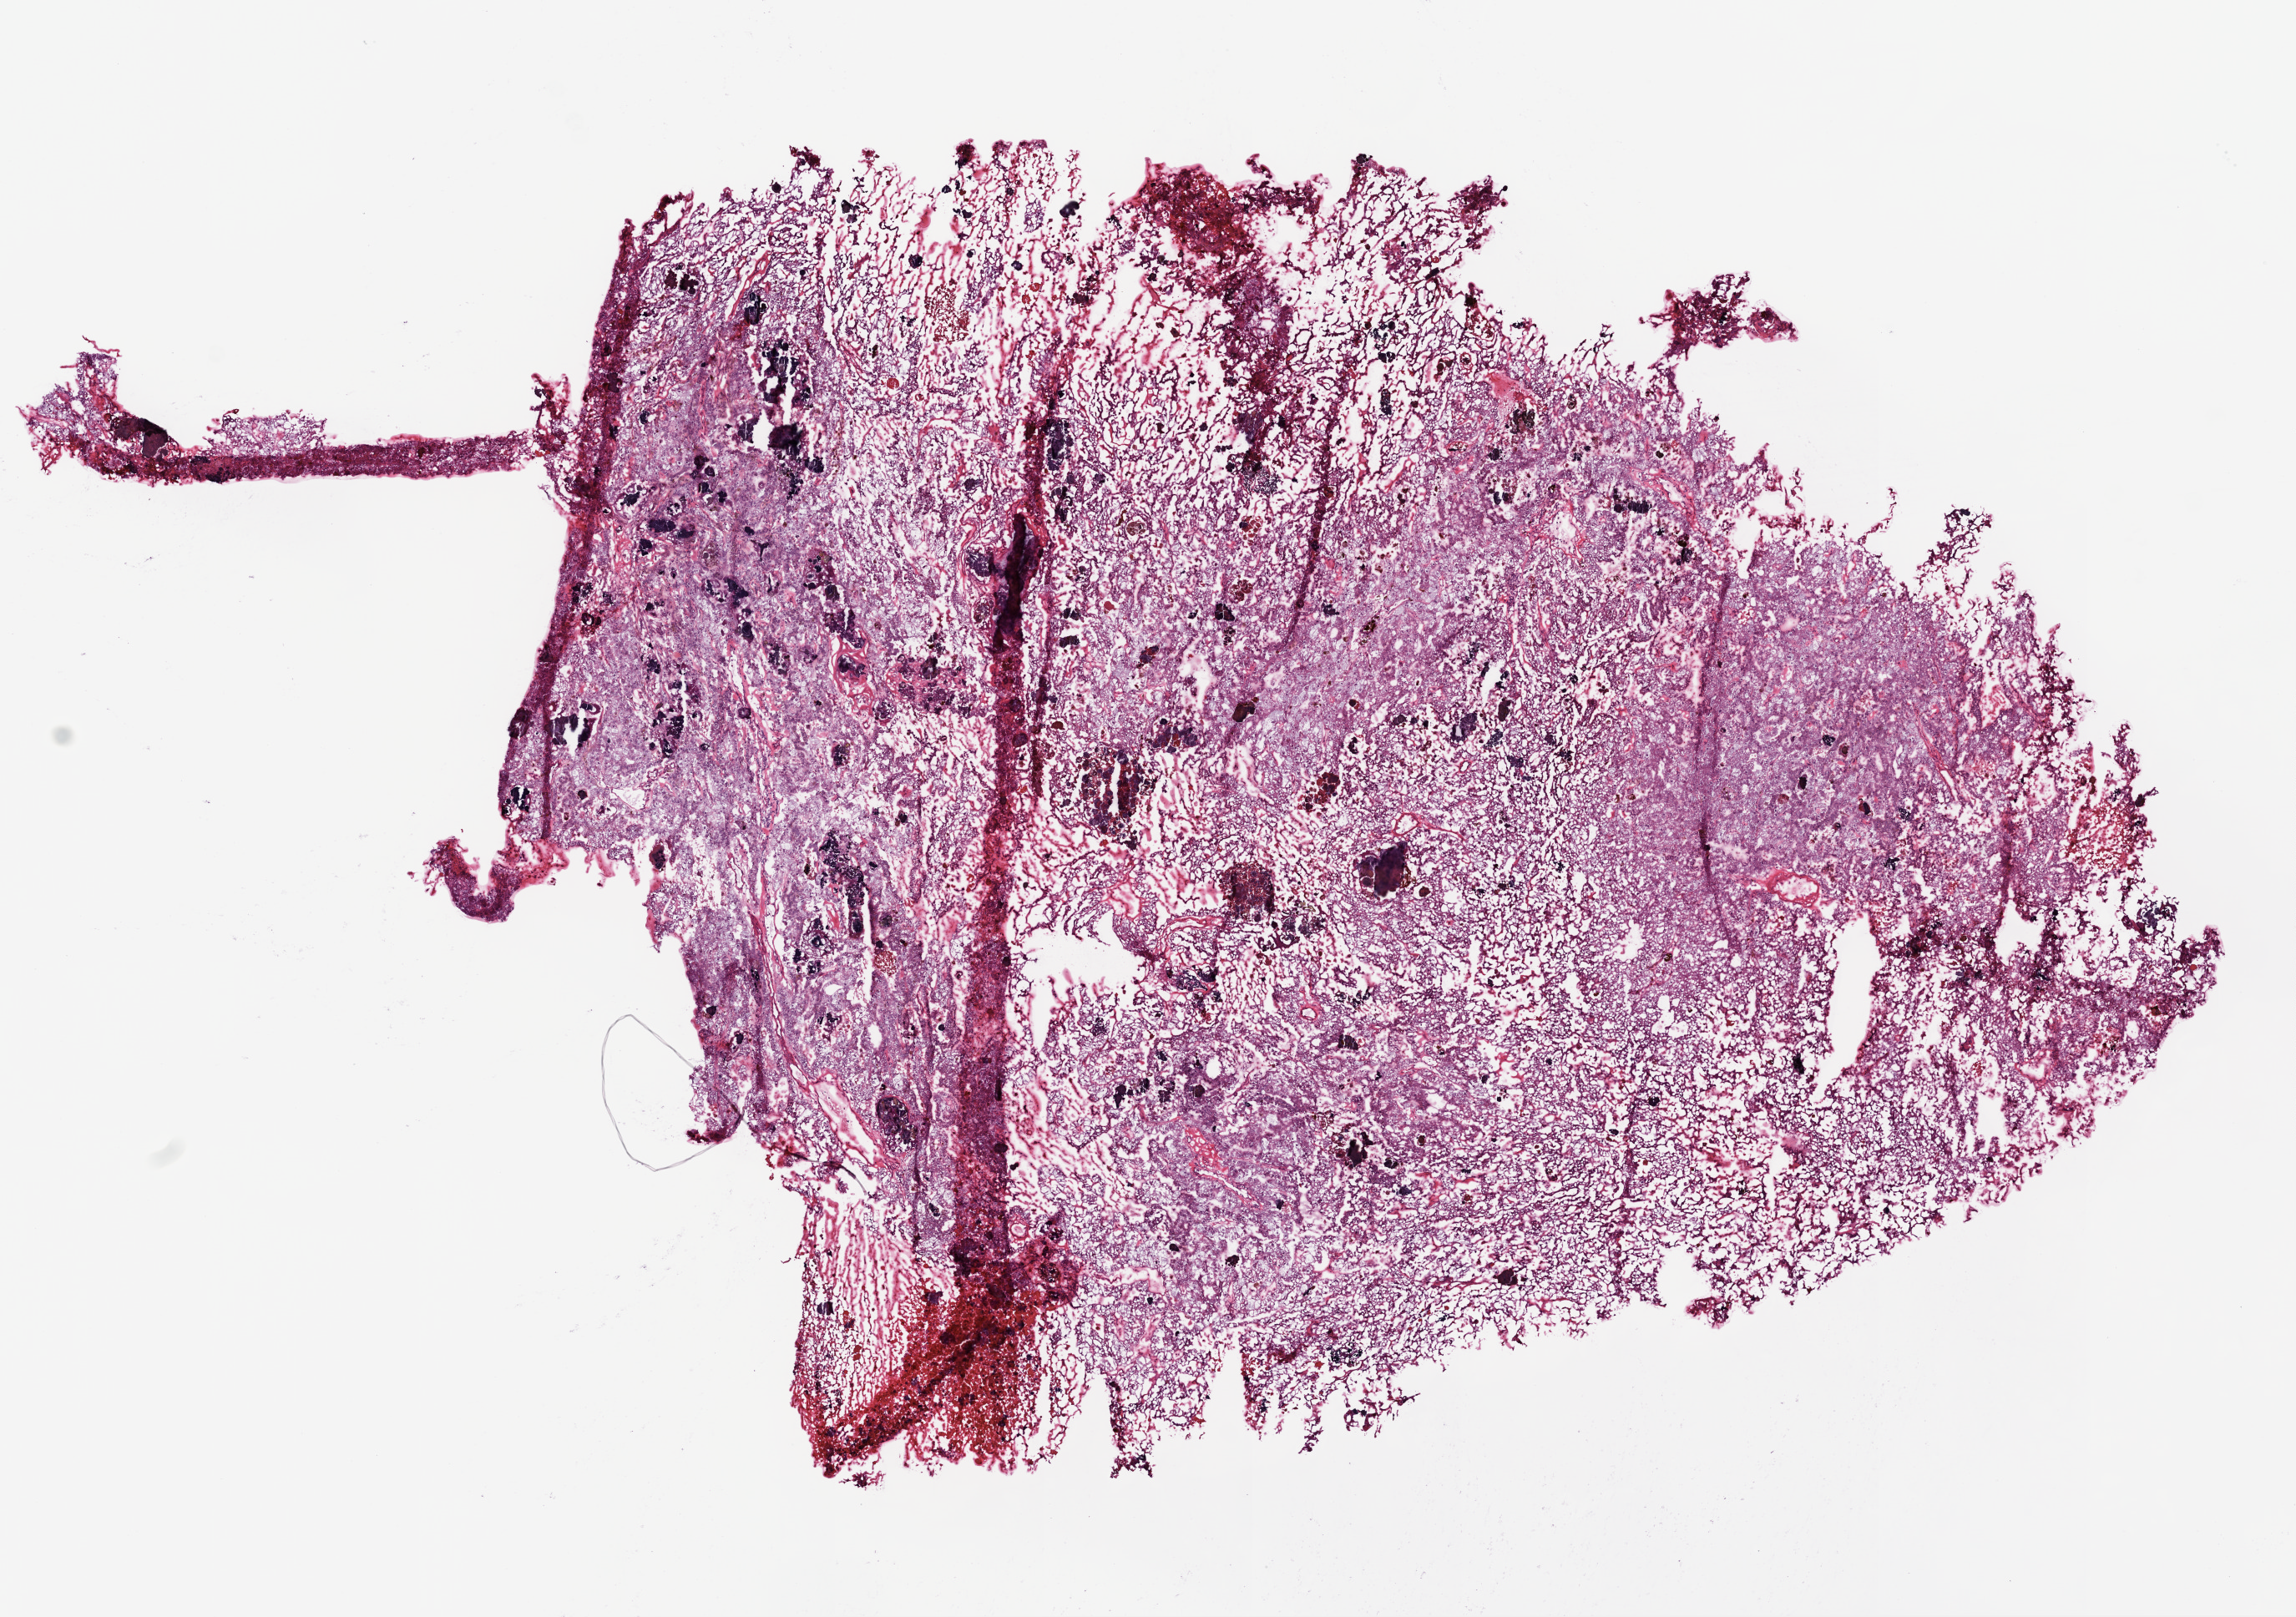
Digitized H&E tissue section (whole slide), shown as a low-resolution overview of the whole scanned area (about 11.0 x 7.8 mm, slide scanned at 20x). Frozen section from the top of the tissue portion. Primary tumour sample from the kidney. Female, age 51 years at initial diagnosis. Histologic grade: G2 (moderately differentiated). Slide review estimates, as recorded: tumour cells 95%, tumour nuclei 80%, normal cells 0%, stromal cells 5%, necrosis 0%.
* AJCC pathologic stage: I
* pathologic diagnosis: Clear cell adenocarcinoma, NOS
* laterality: right